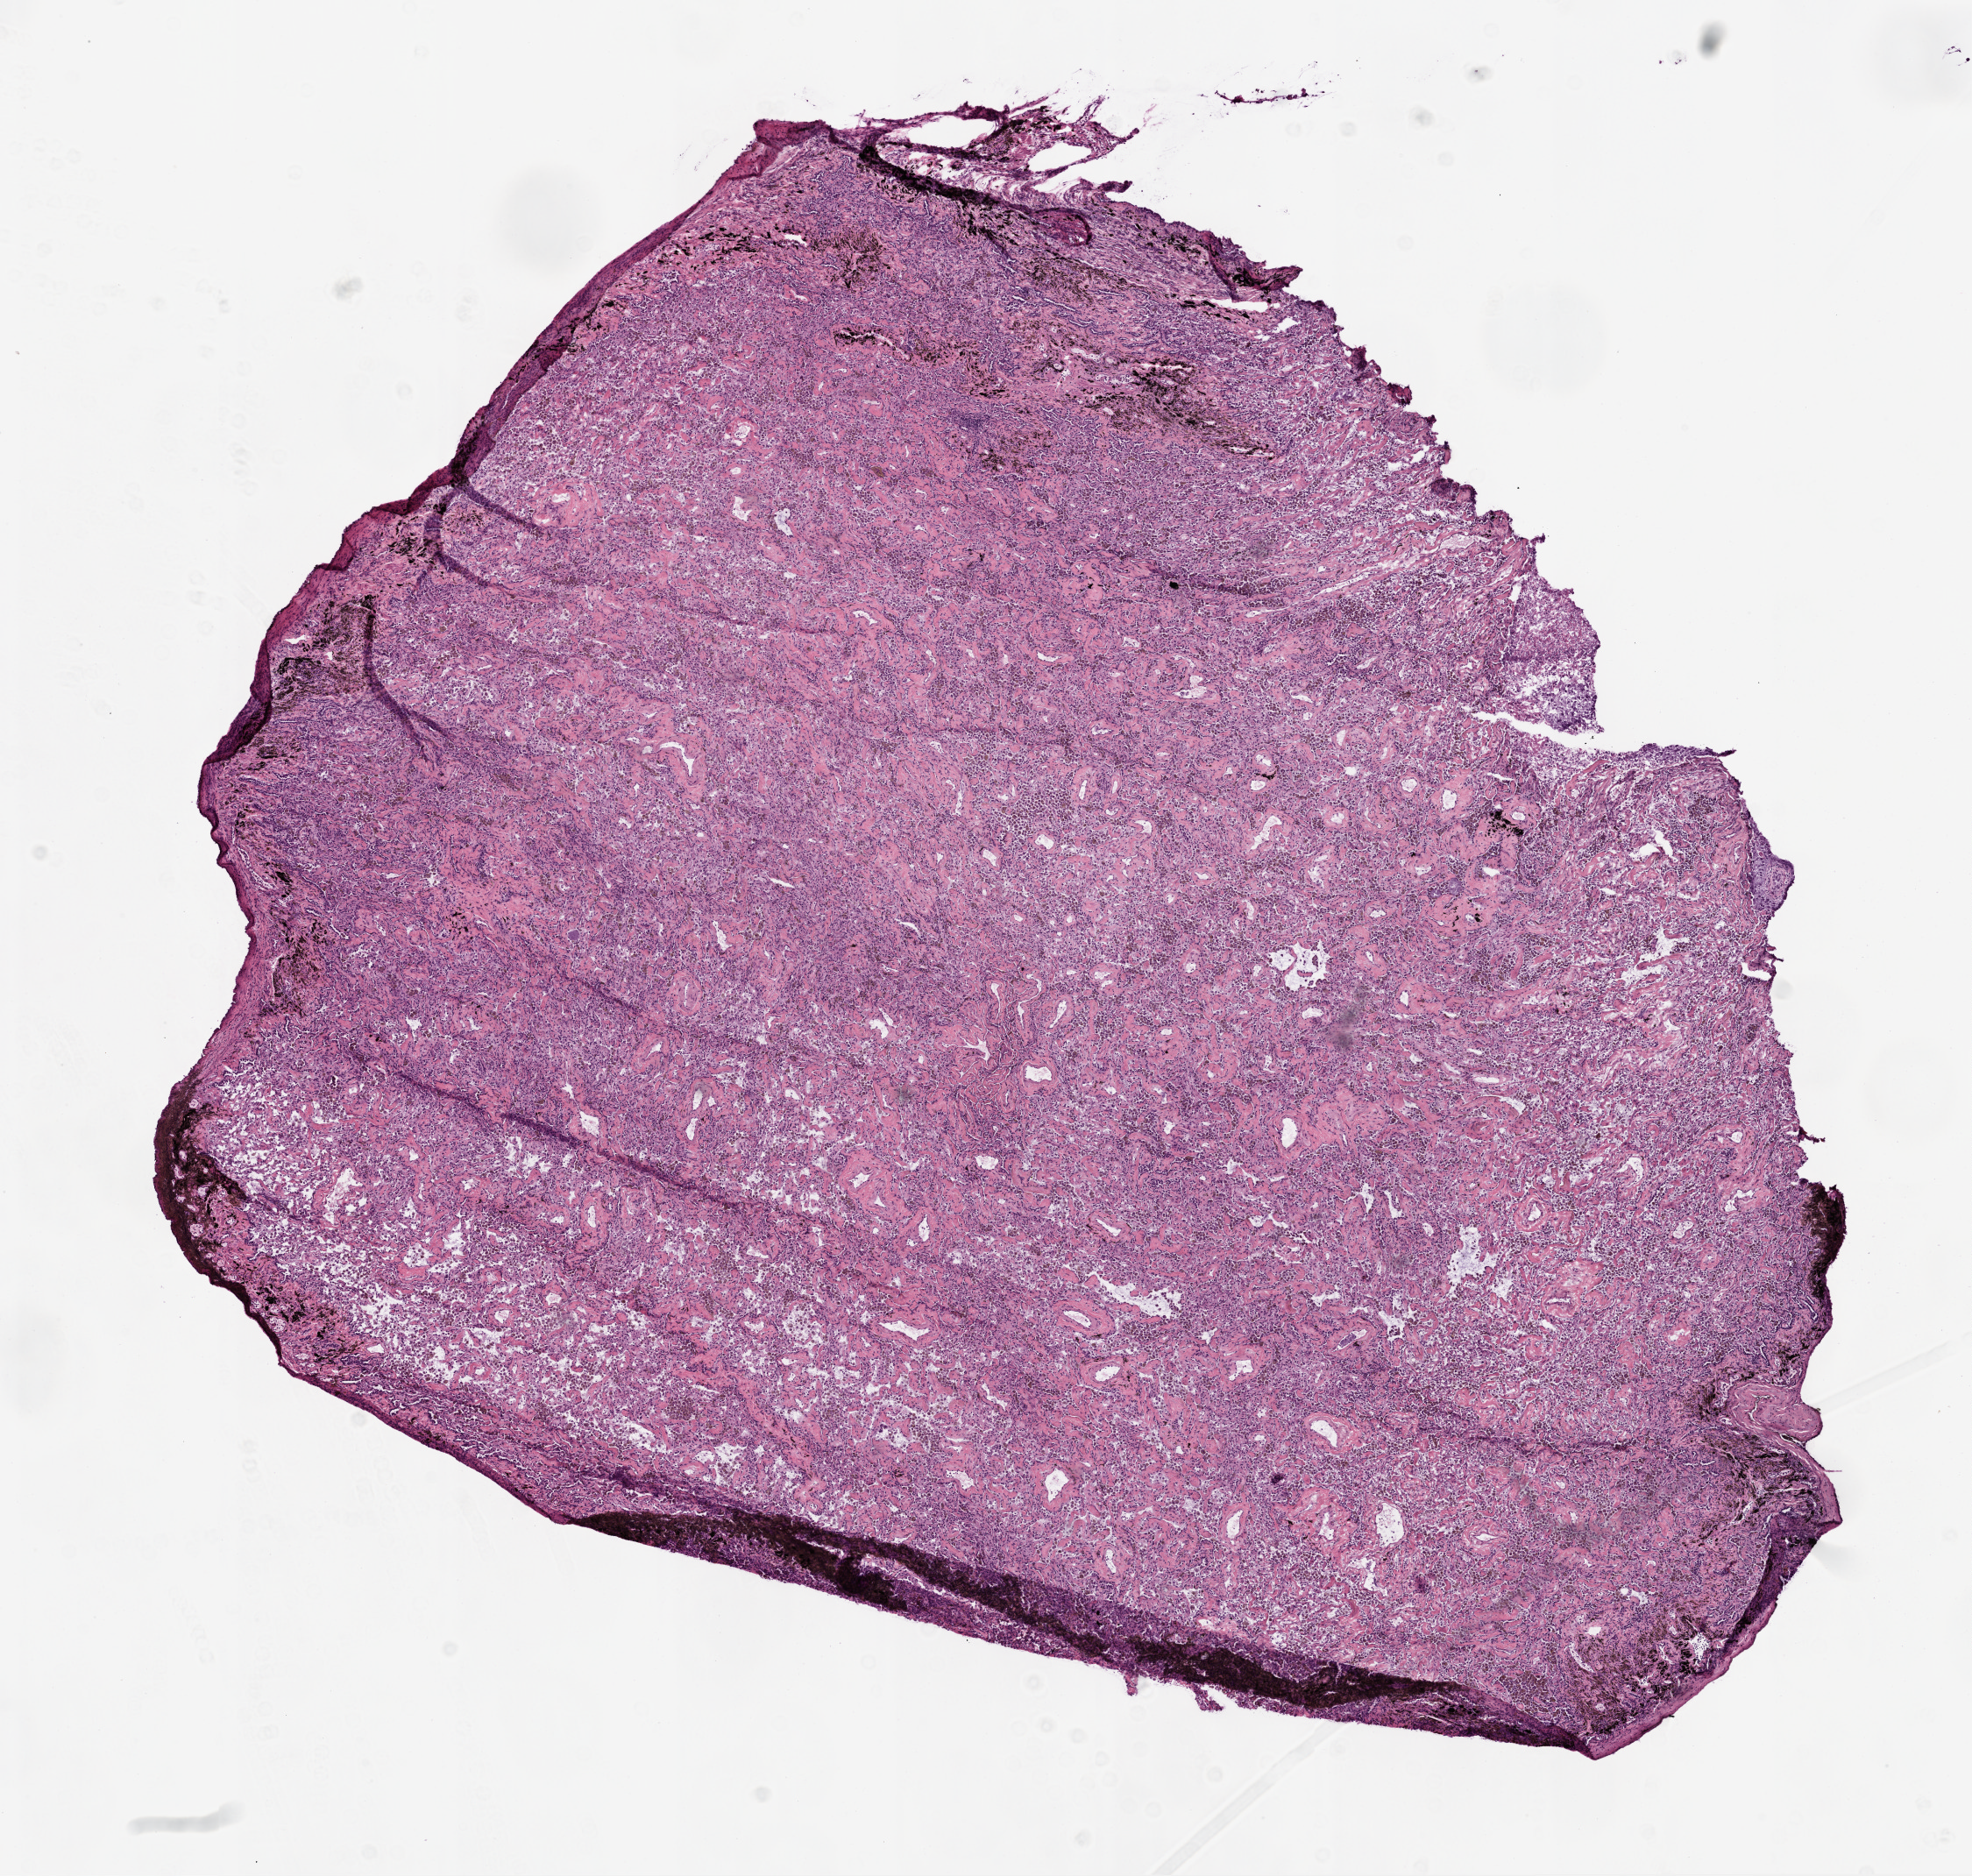
Whole-slide histology image, H&E-stained, a low-resolution overview of the entire scanned area, about 9.0 x 8.6 mm; frozen section; sample: solid tissue normal (non-tumour tissue), lung. Patient: male, age at initial diagnosis 47 years.
- this section: solid tissue normal (non-tumour) sample from the same patient
- patient diagnosis: Squamous cell carcinoma, NOS